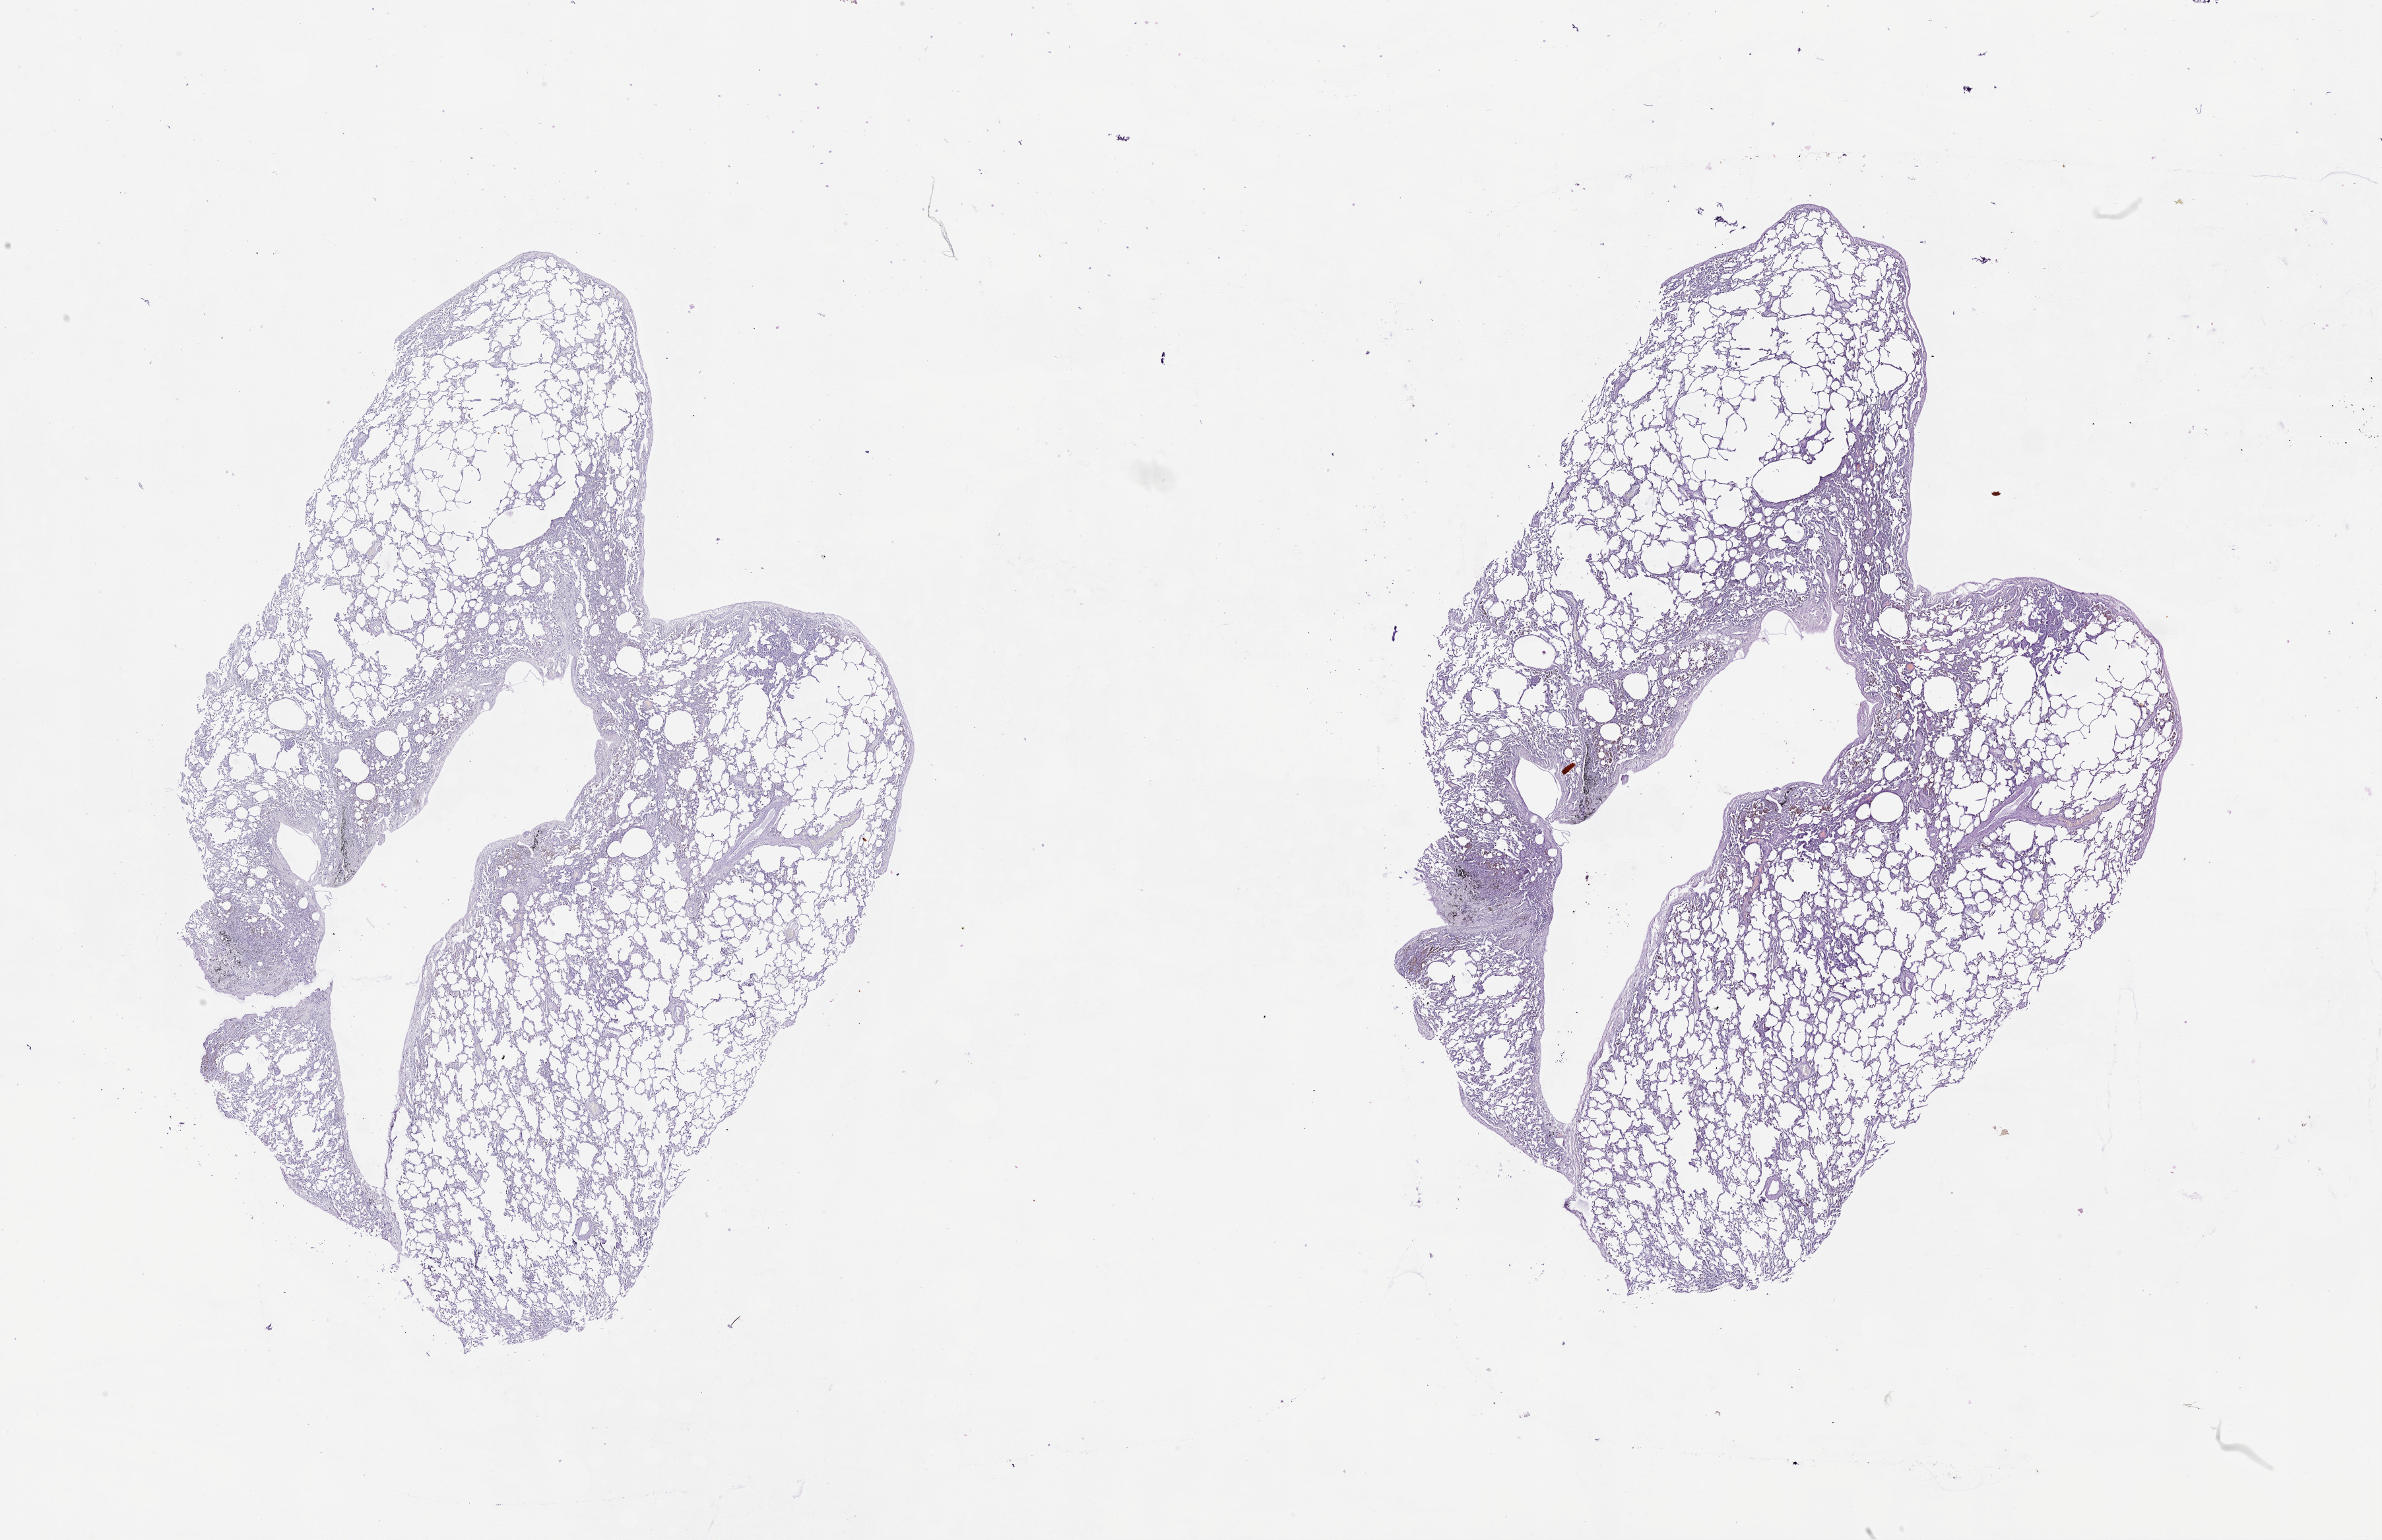
Whole-slide histology image, H&E-stained — shown as a low-resolution overview of the whole scanned area (about 29.1 x 18.8 mm, from a 20x scan), lung, tissue type not recorded.
* patient diagnosis (cohort enrolment): lung adenocarcinoma (lung)